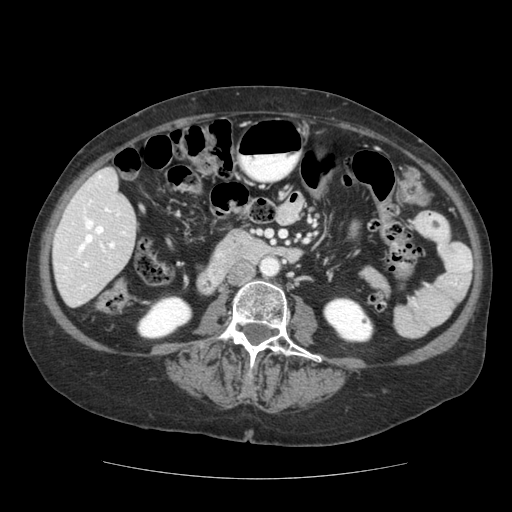
Contrast-enhanced abdominal CT (liver protocol), one axial slice. 140 kVp. Soft-tissue window (W 400 / L 40 HU). 2.5 mm slice thickness. 512 × 512 image matrix. Case-level facts recorded for this patient, not image findings: diagnosis: hepatocellular carcinoma (patient treated with transarterial chemoembolisation; whether this scan precedes or follows treatment is not stated here); TNM stage (as recorded): Stage-I; Child-Pugh class: A; tumour differentiation: moderately-poorly differentiated; tumour size: 7.3 cm.
Outlined on this slice (semi-automatic segmentation, software-assisted and operator-edited):
- liver parenchyma outside the tumour (the mass and vessels are separate outlines, so this box may not span the whole liver): bounding box <52,168,136,306> (left, top, right, bottom; pixels)
- liver vessels: <57,175,126,289>